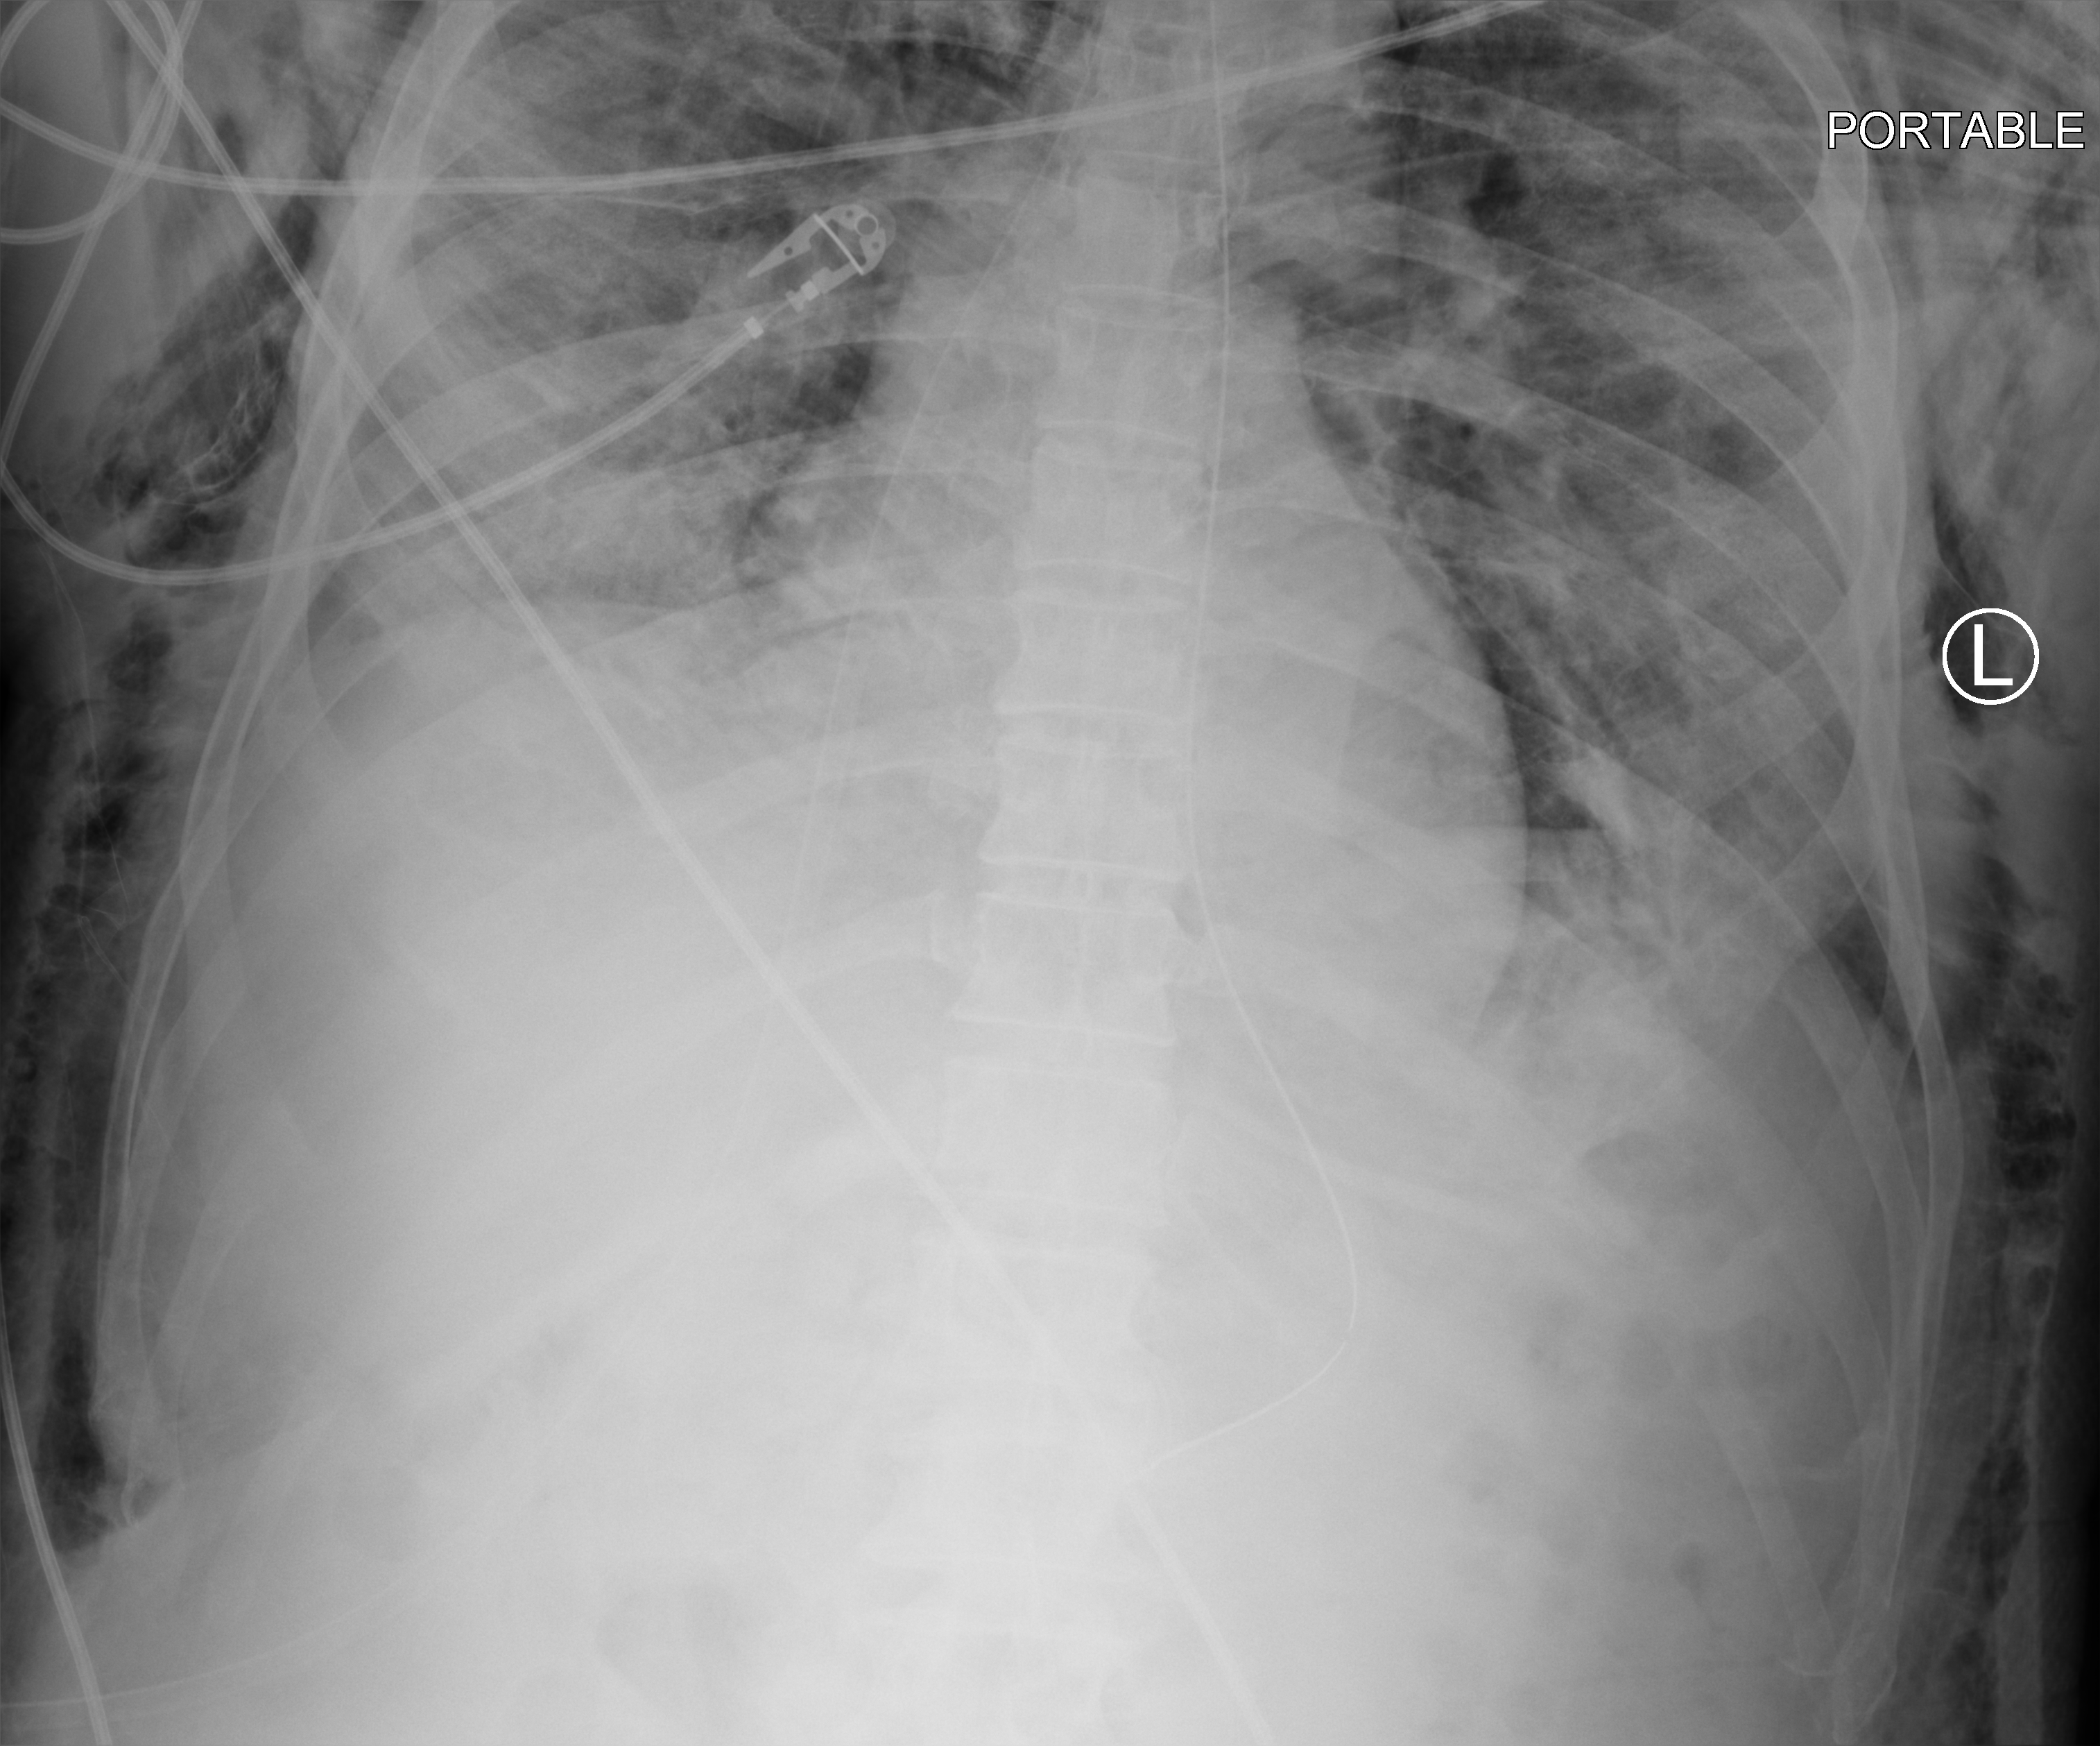
Portable chest radiograph; anteroposterior (AP) projection. Male patient hospitalised with COVID-19, age 60–74 years.
From the hospital-stay record, not from the radiograph (when in the stay this image was taken is not recorded):
- length of hospital stay: 8 days